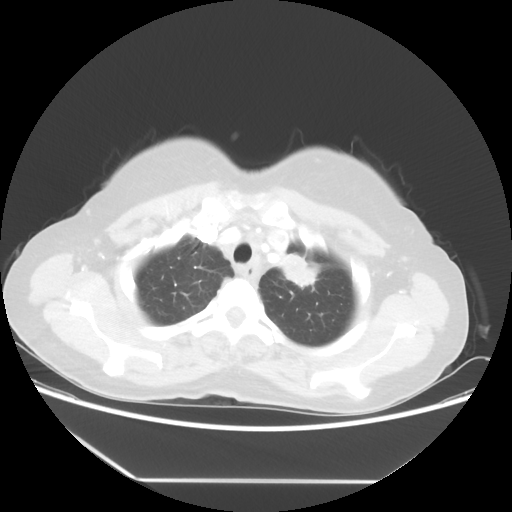
Chest CT, one axial slice; position 45 of 52 along the scan axis; reconstruction kernel STANDARD; lung window (W 1500 / L -600 HU); 5 mm slice thickness; 512 × 512 image matrix, field of view 390 × 390 mm. Female patient, age 50 years. From the clinical record (not read from this slice): clinical TNM (as recorded): T2 N3 M0.
Structures marked on this image (rectangle marked by the reading radiologist):
- lung tumour (recorded histology: adenocarcinoma): bounding box [x1, y1, x2, y2] px = [269, 241, 325, 307]